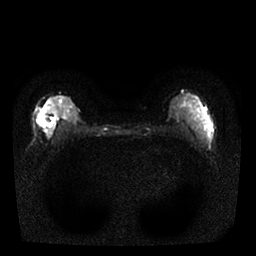
Breast MRI, one axial slice; position 12 of 25 along the scan axis; diffusion-weighted series; image 2 of 4 stored at this slice position (different b-values; order by instance number); 1.5 T; 4 mm slice thickness; 256 × 256 image matrix. Female patient.
Structures marked on this image (outlined manually by an expert reader):
- tumour on diffusion-weighted imaging: bounding box <38,113,54,128> (left, top, right, bottom; pixels)